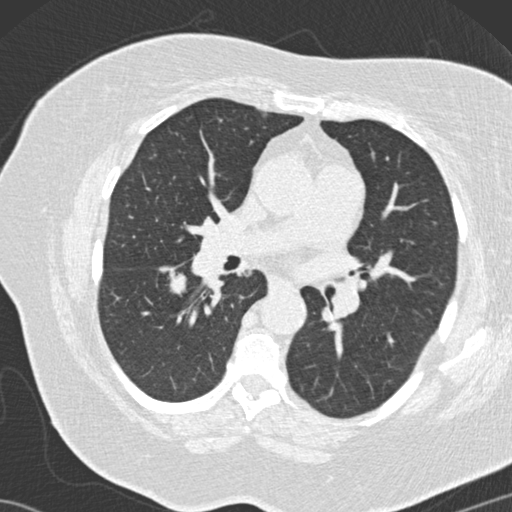
Low-dose screening chest CT, one axial slice. Position 76 of 146 along the scan axis. 120 kVp. Lung window (W 1500 / L -600 HU). 2 mm slice thickness. 512 × 512 image matrix.
Structures marked on this image (outlined manually by an expert reader):
- lesion 4 (tumor, lower lobe of right lung): box from (x=170, y=274) to (x=188, y=294) px